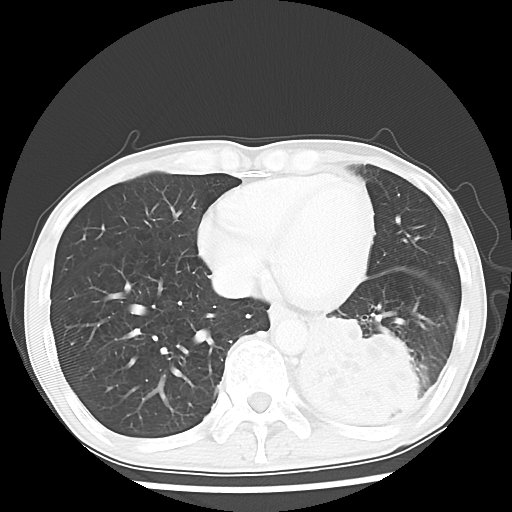
Chest CT, one axial slice; 120 kVp; lung window (W 1500 / L -600 HU); 512 × 512 image matrix, field of view 313 × 313 mm. Male patient, age 68 years. From the clinical record (not read from this slice): clinical TNM (as recorded): T4 N0 M0.
Outlined on this slice (bounding box drawn by a radiologist):
- lung tumour (recorded histology: squamous cell carcinoma): box from (x=291, y=310) to (x=425, y=420) px